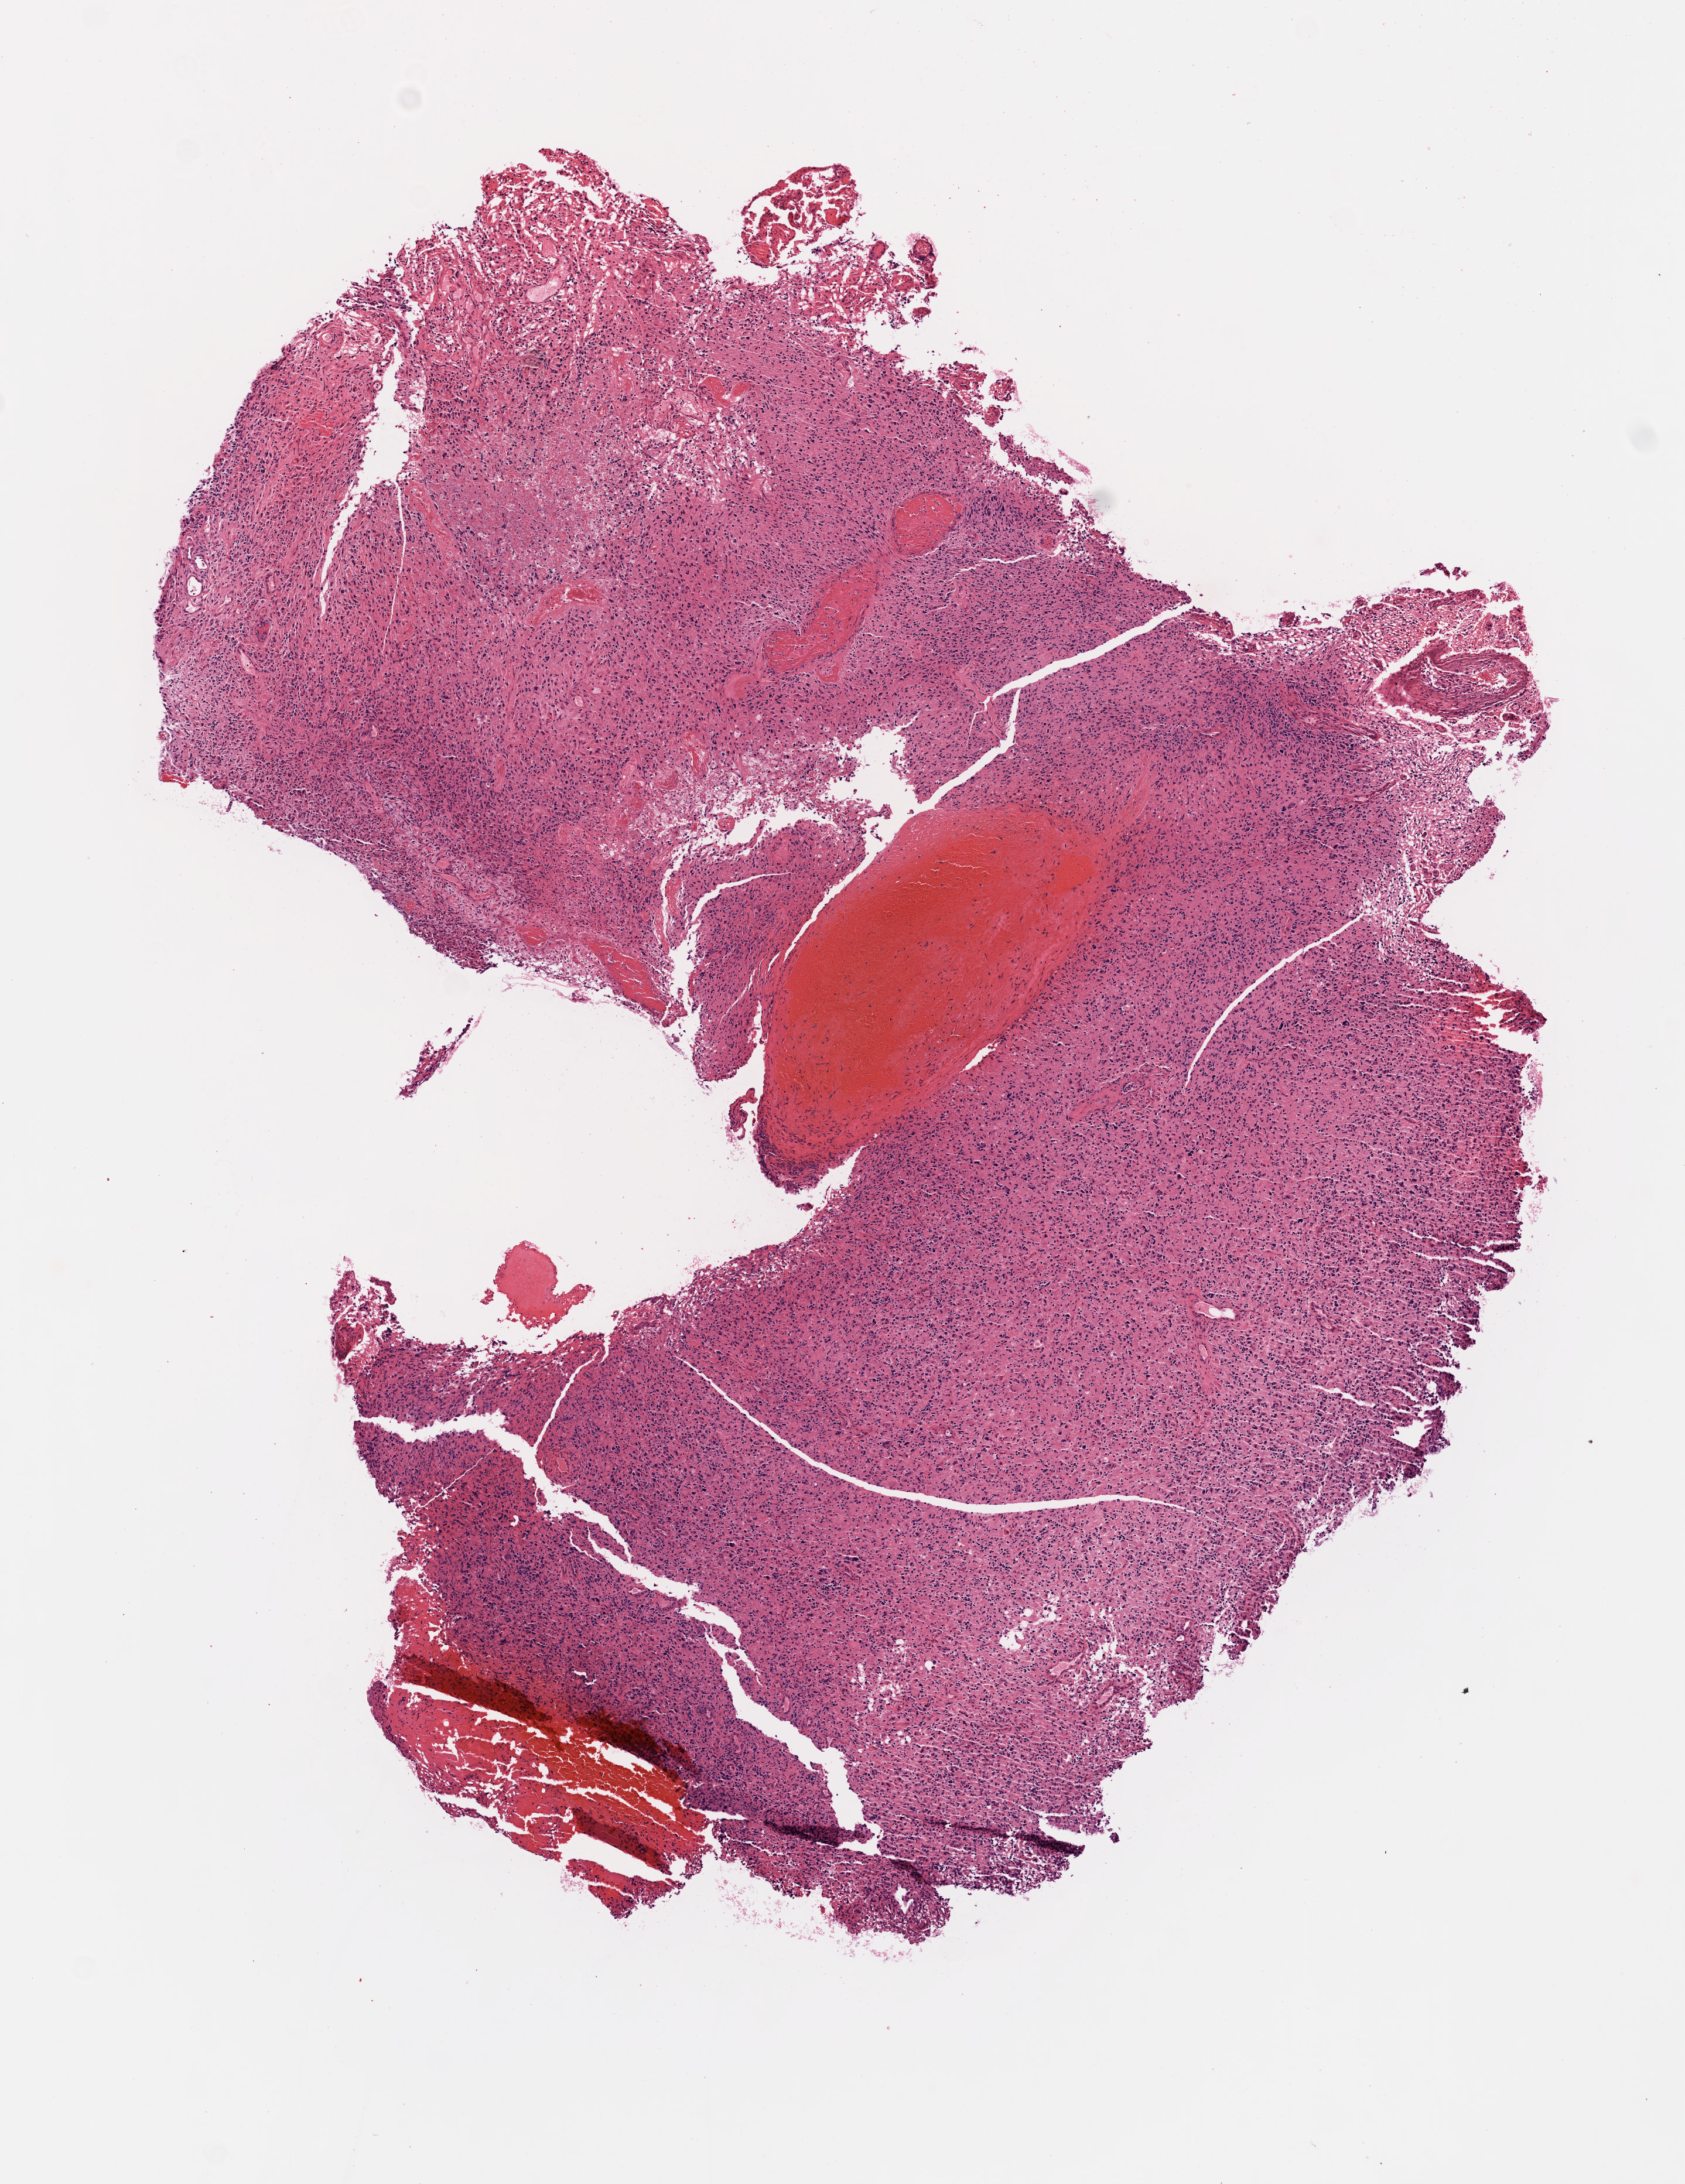
H&E-stained whole-slide image — a low-resolution overview of the entire scanned area, about 5.8 x 7.5 mm; formalin-fixed paraffin-embedded (FFPE) diagnostic section; brain, primary tumour sample. Patient: male, age at initial diagnosis 57 years.
Diagnosis: Glioblastoma.